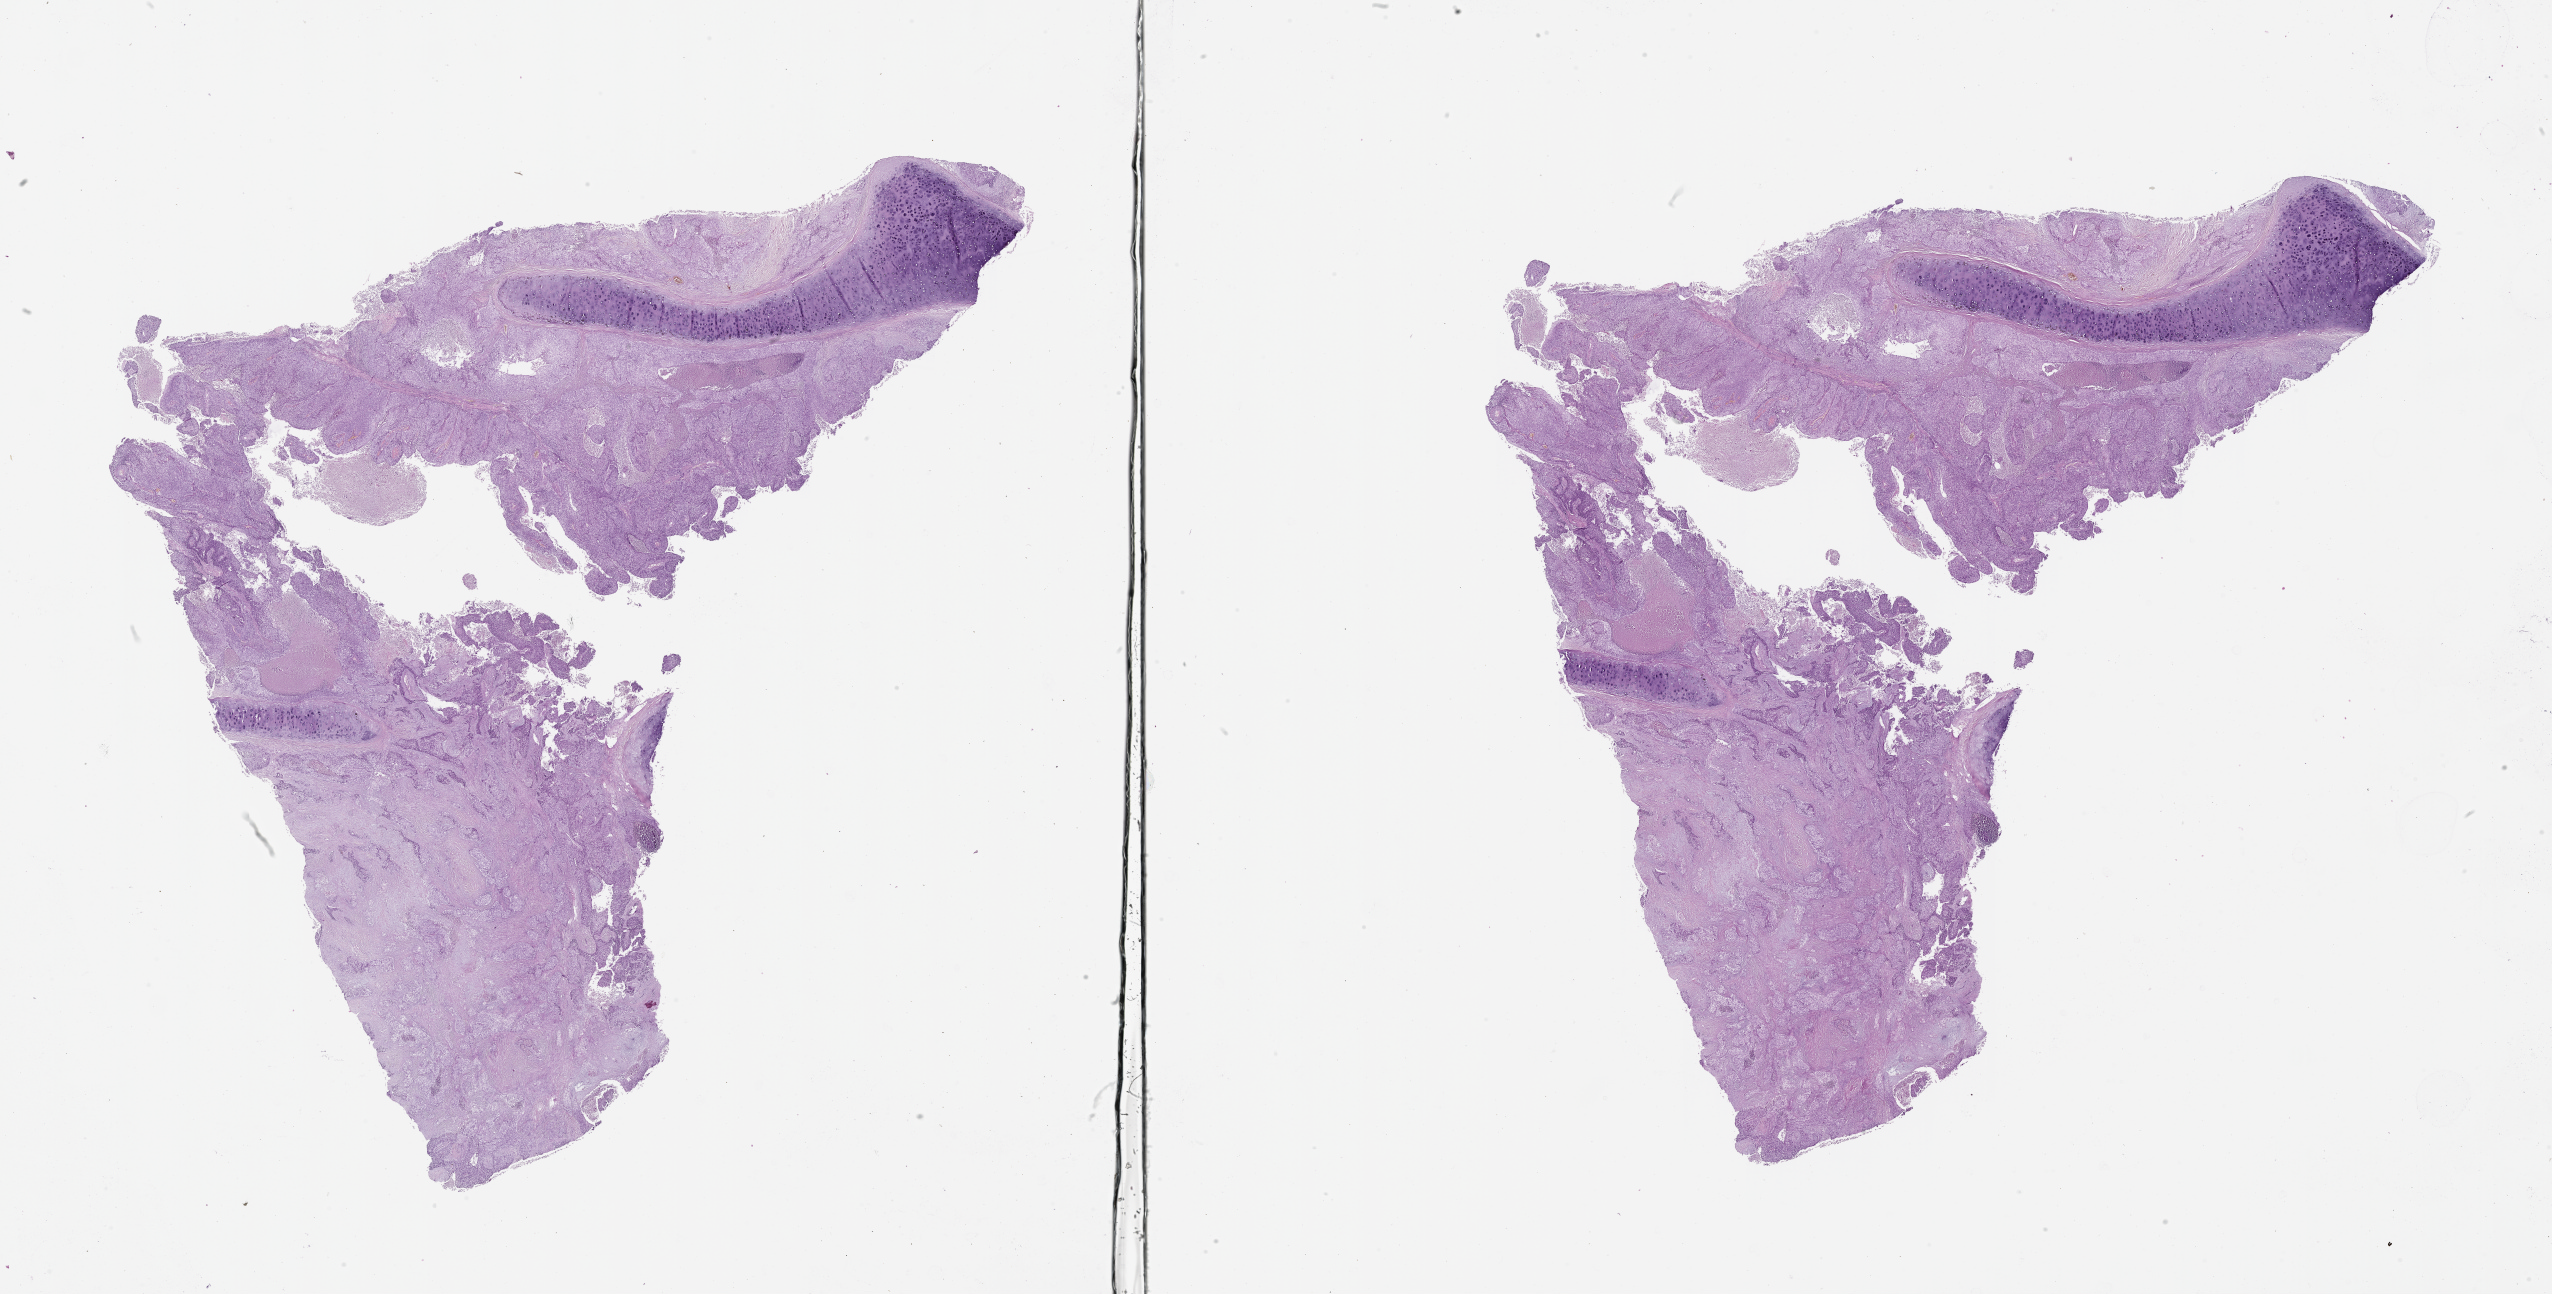
Hematoxylin and eosin (H&E) stained whole-slide image — low-resolution overview of the scanned area, about 41.1 x 20.8 mm (from a 20x scan); lung, tumour tissue. Male, 65 y/o.
Patient diagnosis (cohort enrolment): squamous cell carcinoma (lung).